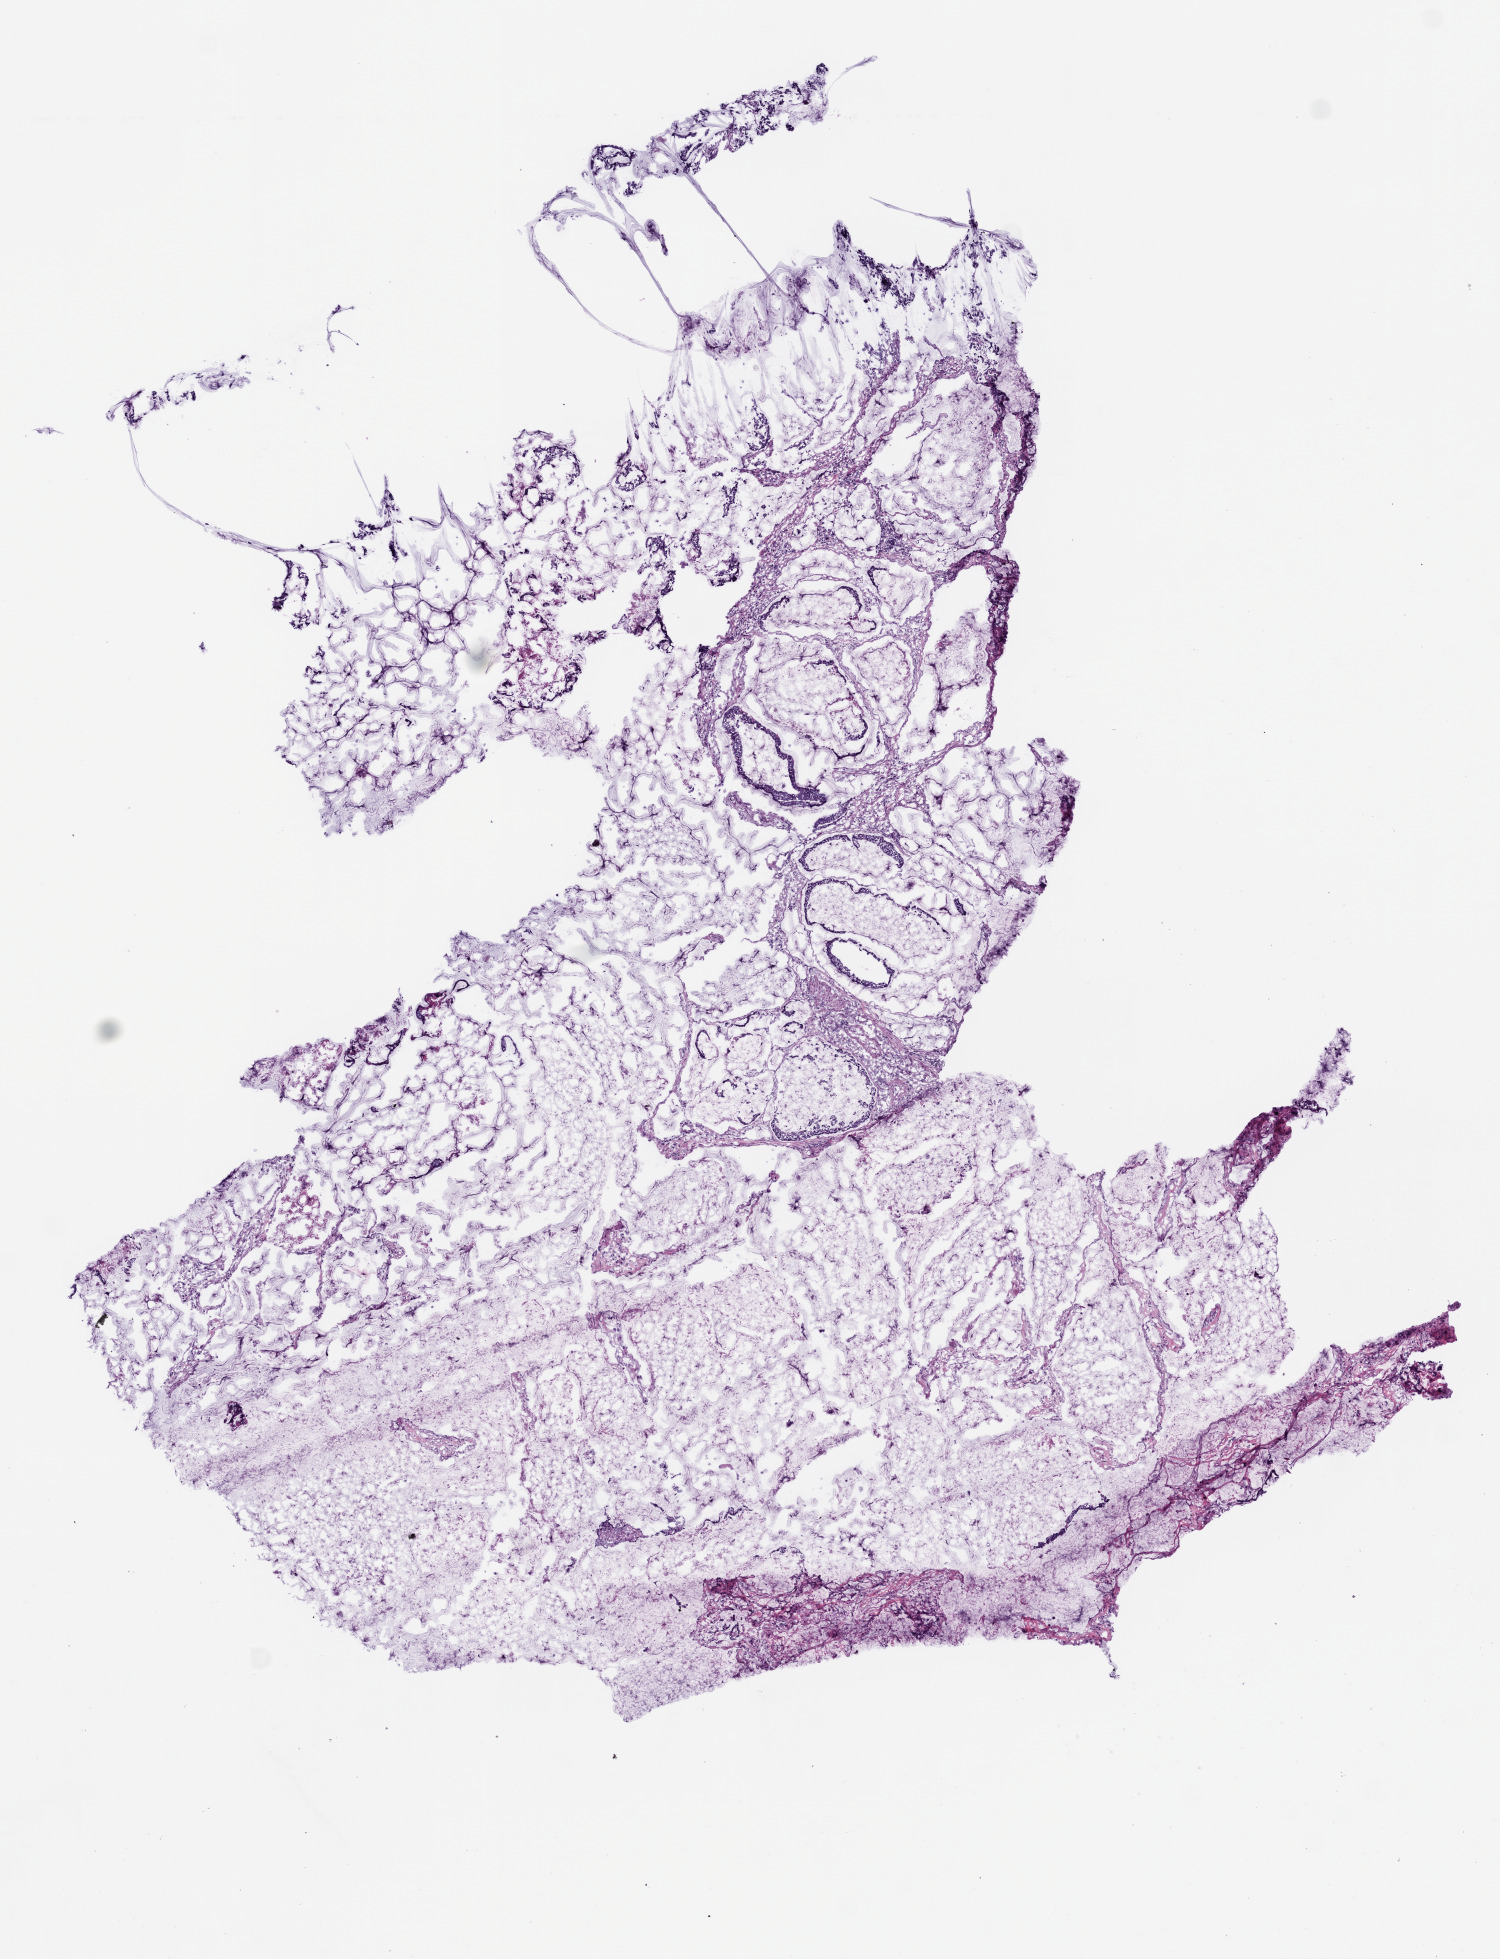
H&E whole-slide image, whole scanned area (about 6.0 x 7.9 mm, slide scanned at 20x) shown as a low-resolution overview, frozen section from the top of the tissue portion, stomach, primary tumour sample. Male, age 72 years at initial diagnosis. Histologic grade: G3 (poorly differentiated). Composition of this section per pathologist review: tumour cells 95%, tumour nuclei 85%, normal cells 0%, stromal cells 5%, necrosis 0%.
Pathologic diagnosis: Mucinous adenocarcinoma (cardia, NOS). AJCC pathologic stage: II (6th edition).